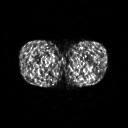
FDG PET of an extremity soft-tissue mass (from a PET/CT study), one axial slice. Slice 230 of 267 in the series (ordered by position). 3.27 mm slice thickness. 128 × 128 image matrix. Patient: male, 27 years. From the clinical record (not read from this slice): histological type: extraskeletal osteosarcoma; grade: high; site of the primary tumour: left adductur.
Annotated regions visible in this slice (expert contour drawn on MRI and transferred to this co-registered scan by the dataset authors):
- gross tumour volume (mass): box from (x=67, y=60) to (x=93, y=78) px